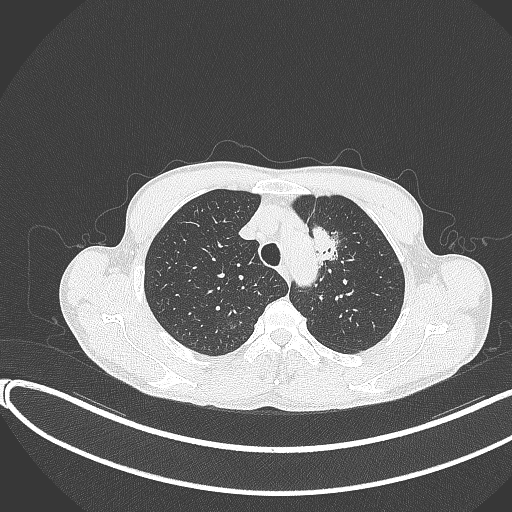
Chest CT, one axial slice. Slice 304 of 374 in the series (ordered by position). Reconstruction kernel B70f. 120 kVp. Lung window (W 1500 / L -600 HU). 512 × 512 image matrix, field of view 400 × 400 mm. Patient: male, 58 years. Case-level facts recorded for this patient, not image findings: clinical TNM (as recorded): T1c N1 M0.
Structures marked on this image (bounding box drawn by a radiologist):
- lung tumour (recorded histology: adenocarcinoma): box from (x=301, y=218) to (x=345, y=264) px